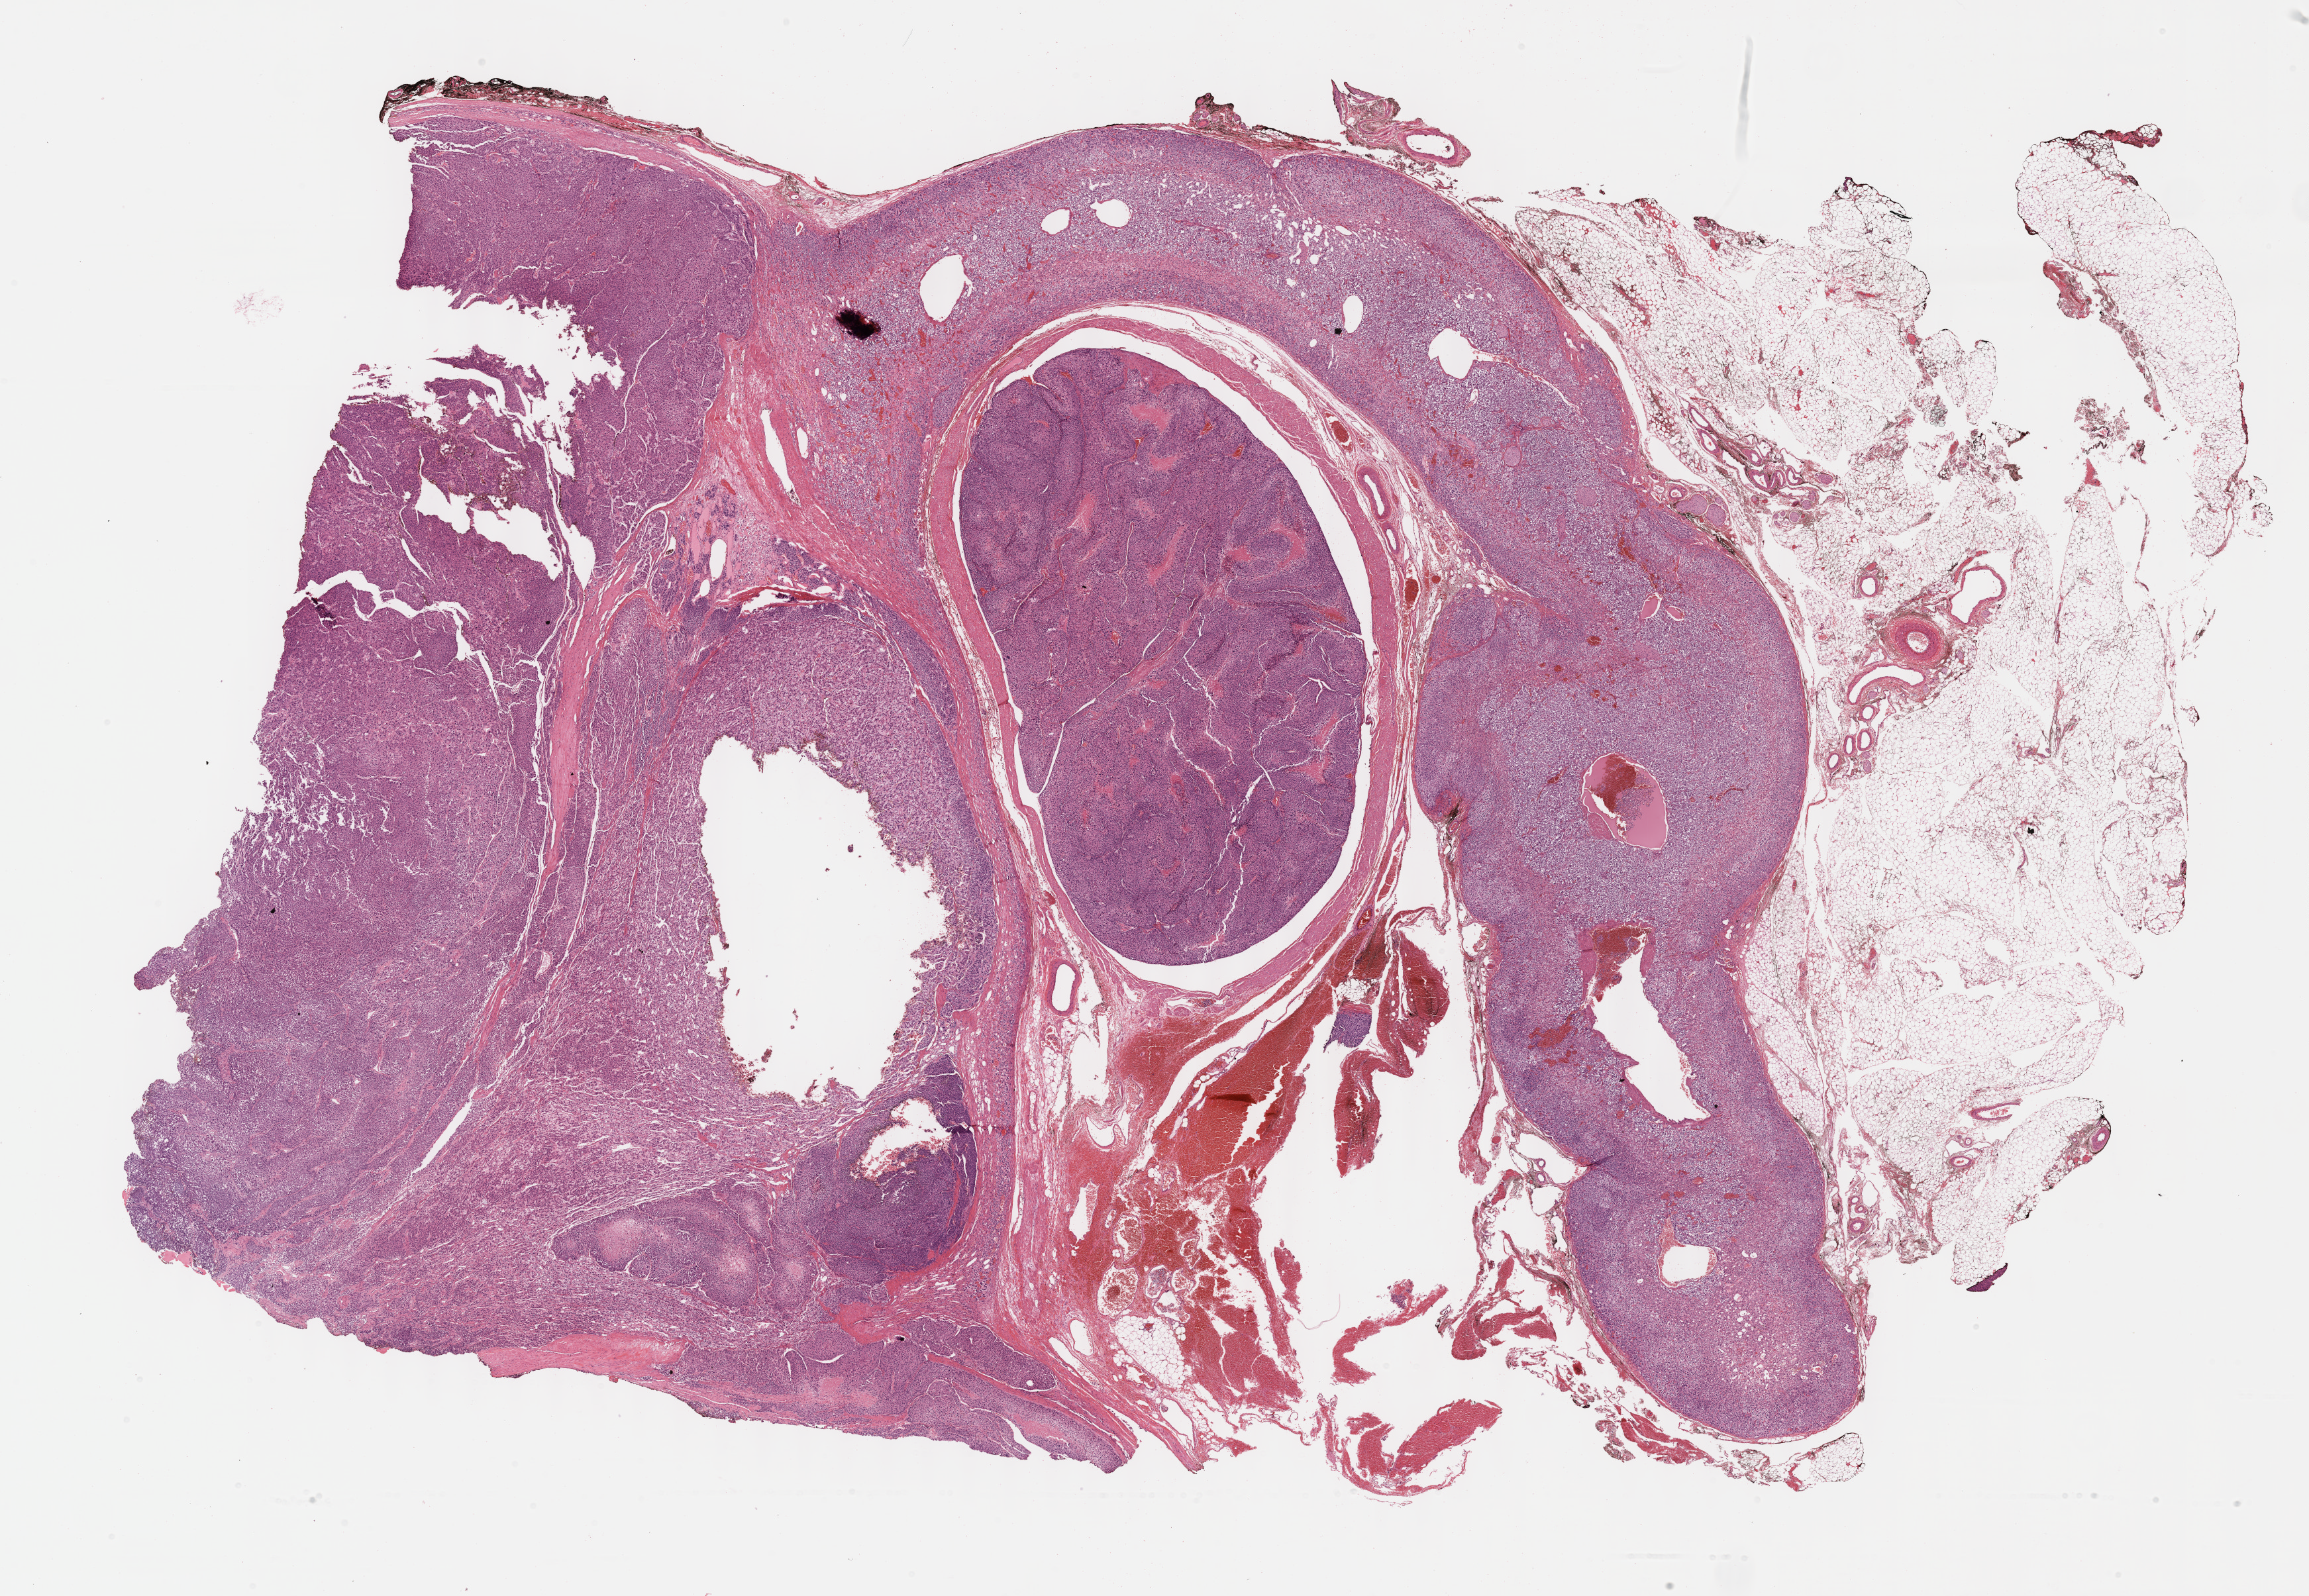
Whole-slide histology image, H&E — a low-resolution overview of the entire scanned area, about 28.2 x 19.5 mm (from a 40x scan). Formalin-fixed paraffin-embedded (FFPE) diagnostic section. Adrenal cortex, primary tumour sample. Female, age 25 years at initial diagnosis.
- laterality: left
- pathologic diagnosis: Adrenal cortical carcinoma (cortex of adrenal gland)